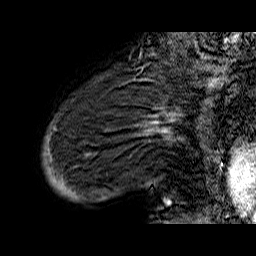
Breast MRI (dynamic contrast-enhanced), one sagittal slice. Position 8 of 60 along the scan axis. Dynamic contrast-enhanced series, time point 2 of 6 at this slice position (early post-contrast). 1.5 T. TE 6.5 ms, TR 32.9 ms. 4 mm slice thickness. 256 × 256 image matrix, field of view 200 × 200 mm. Female patient. Case-level facts recorded for this patient, not image findings: setting: breast cancer imaged before/during neoadjuvant chemotherapy; receptor status: HR-positive, HER2-negative.
Structures marked on this image (semi-automatically segmented with operator editing):
- analysis volume of interest (the breast-tissue region the enhancement analysis was run in; not a lesion): bounding box <43,74,176,210> (left, top, right, bottom; pixels)
- tumour enhancement mask (voxels above the 100 % enhancement threshold inside the analysis volume of interest): <154,117,171,205>